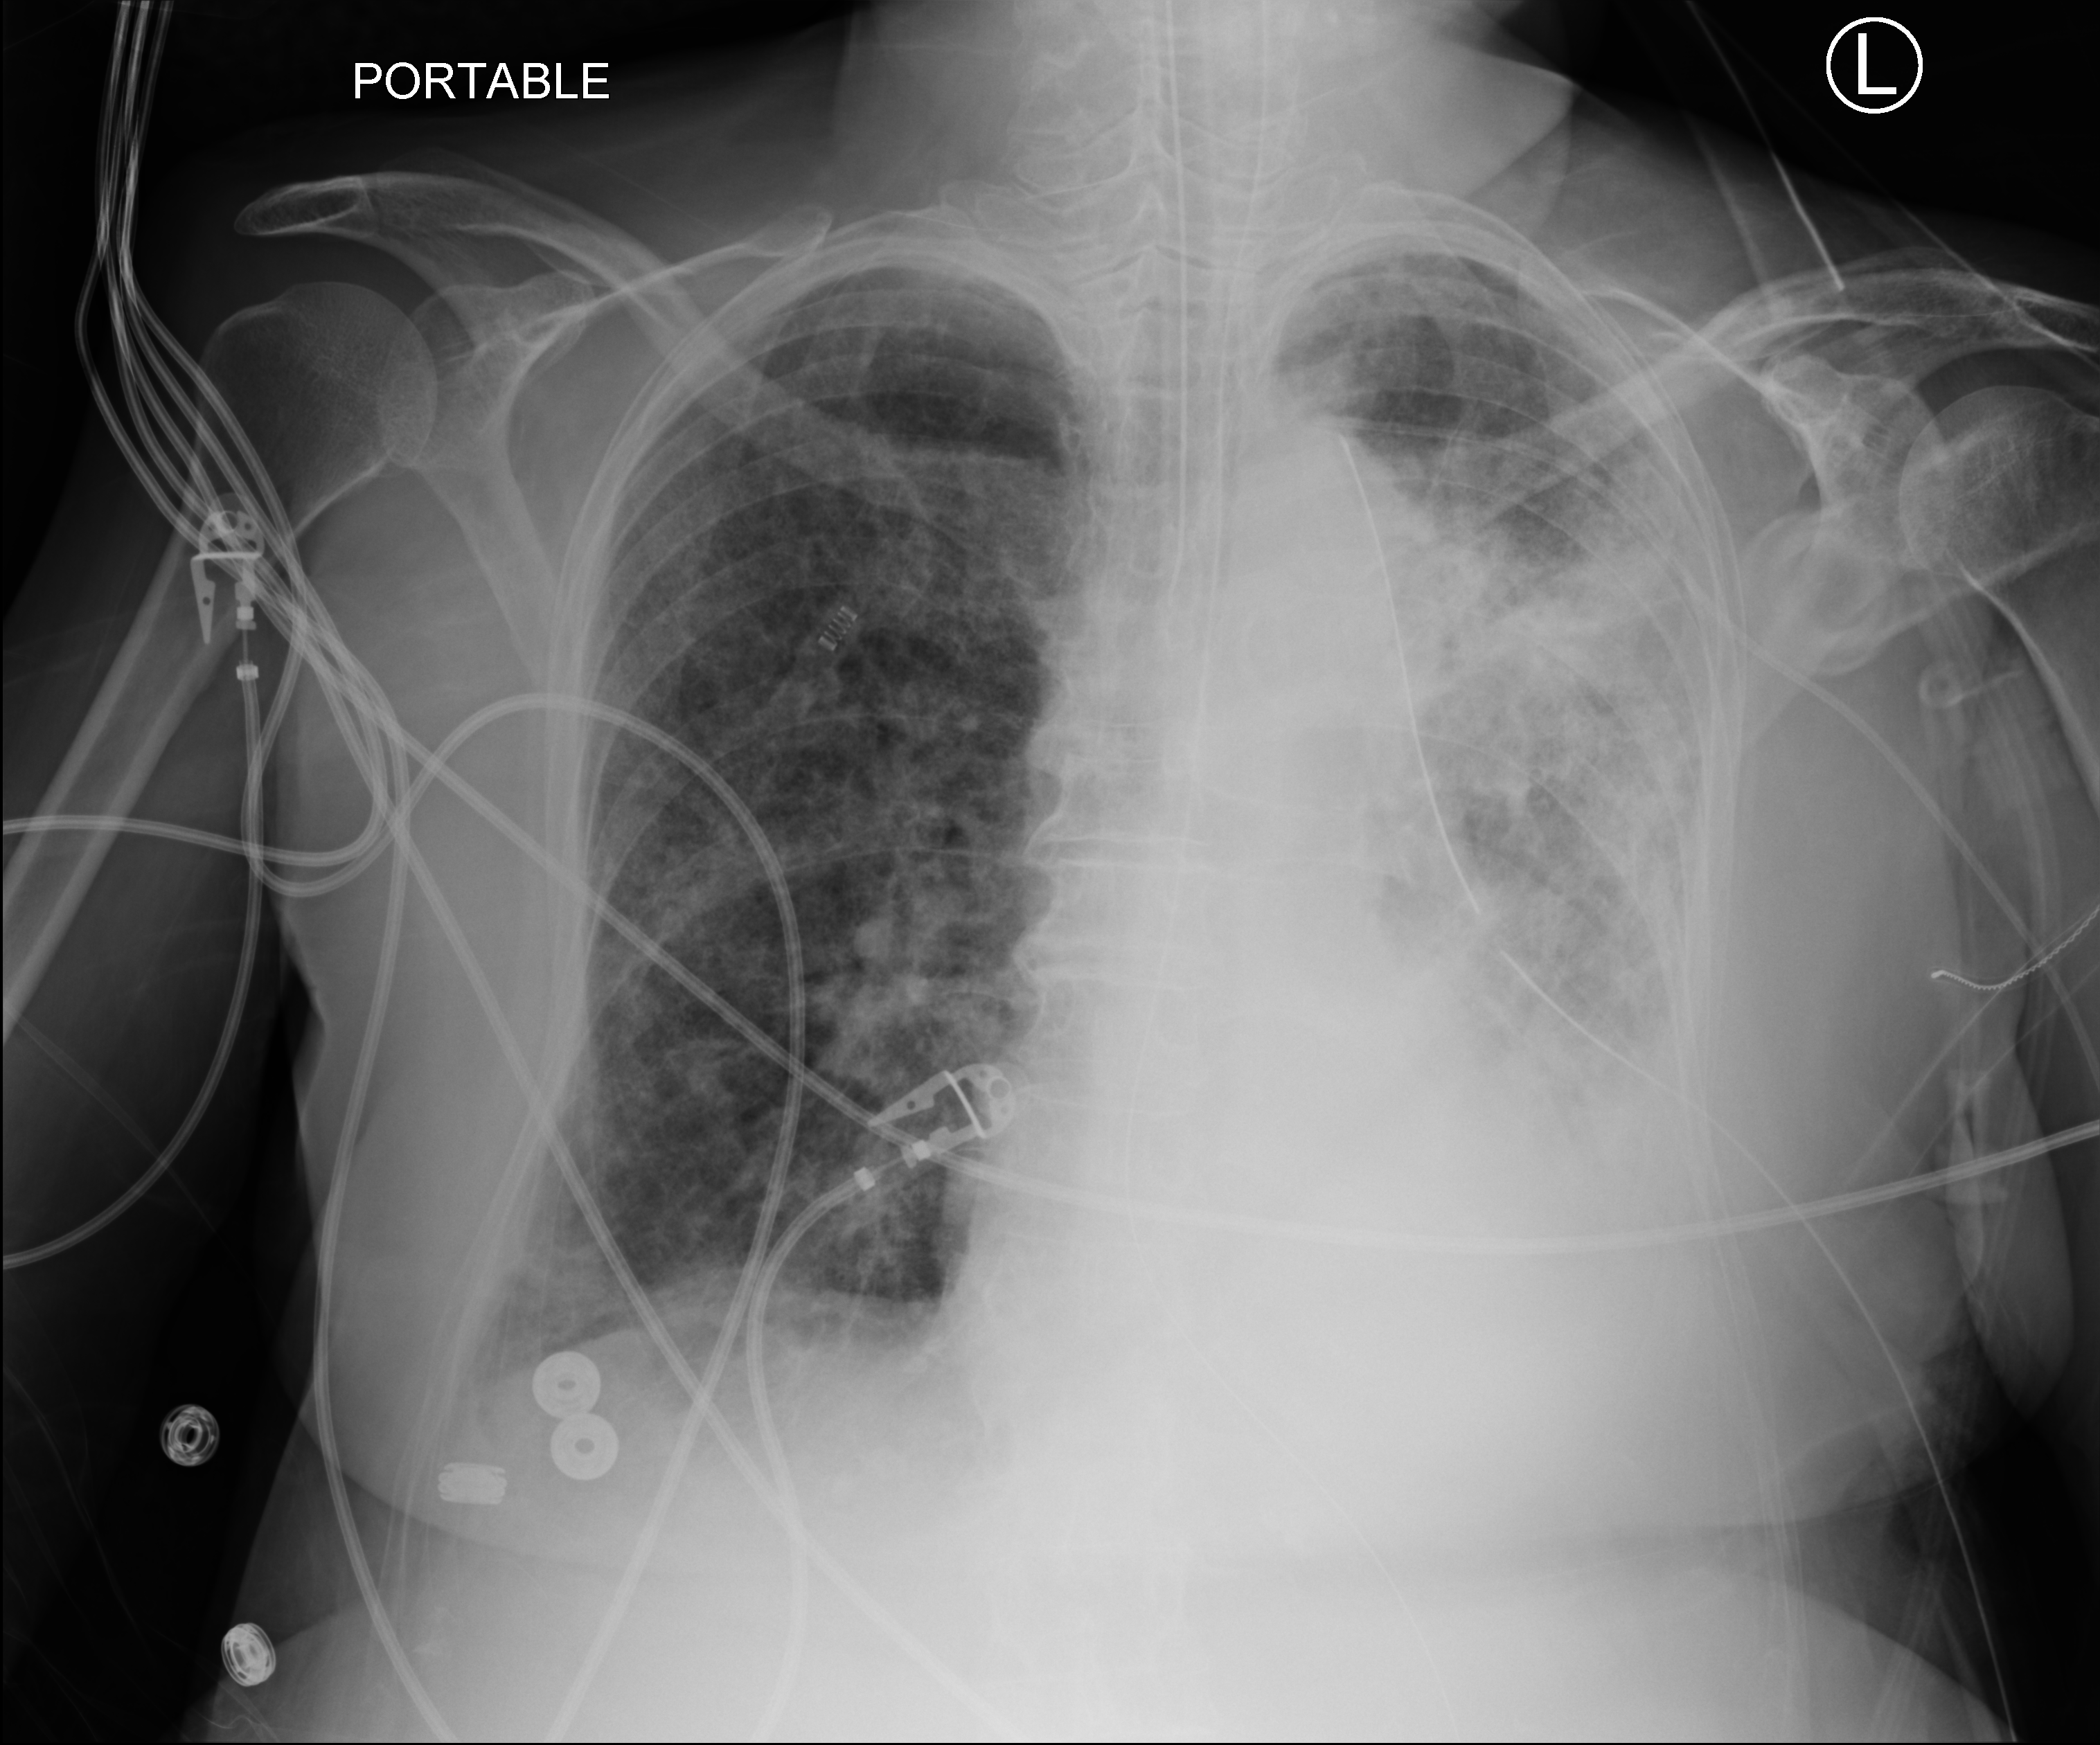
Bedside chest radiograph (computed radiography); anteroposterior (AP) projection. Female patient hospitalised with COVID-19, age 75–90 years.
Admission-level facts for this patient (not findings on this image; timing relative to this image not recorded): mechanically ventilated during this hospital stay: yes; diabetes (admission record): no.